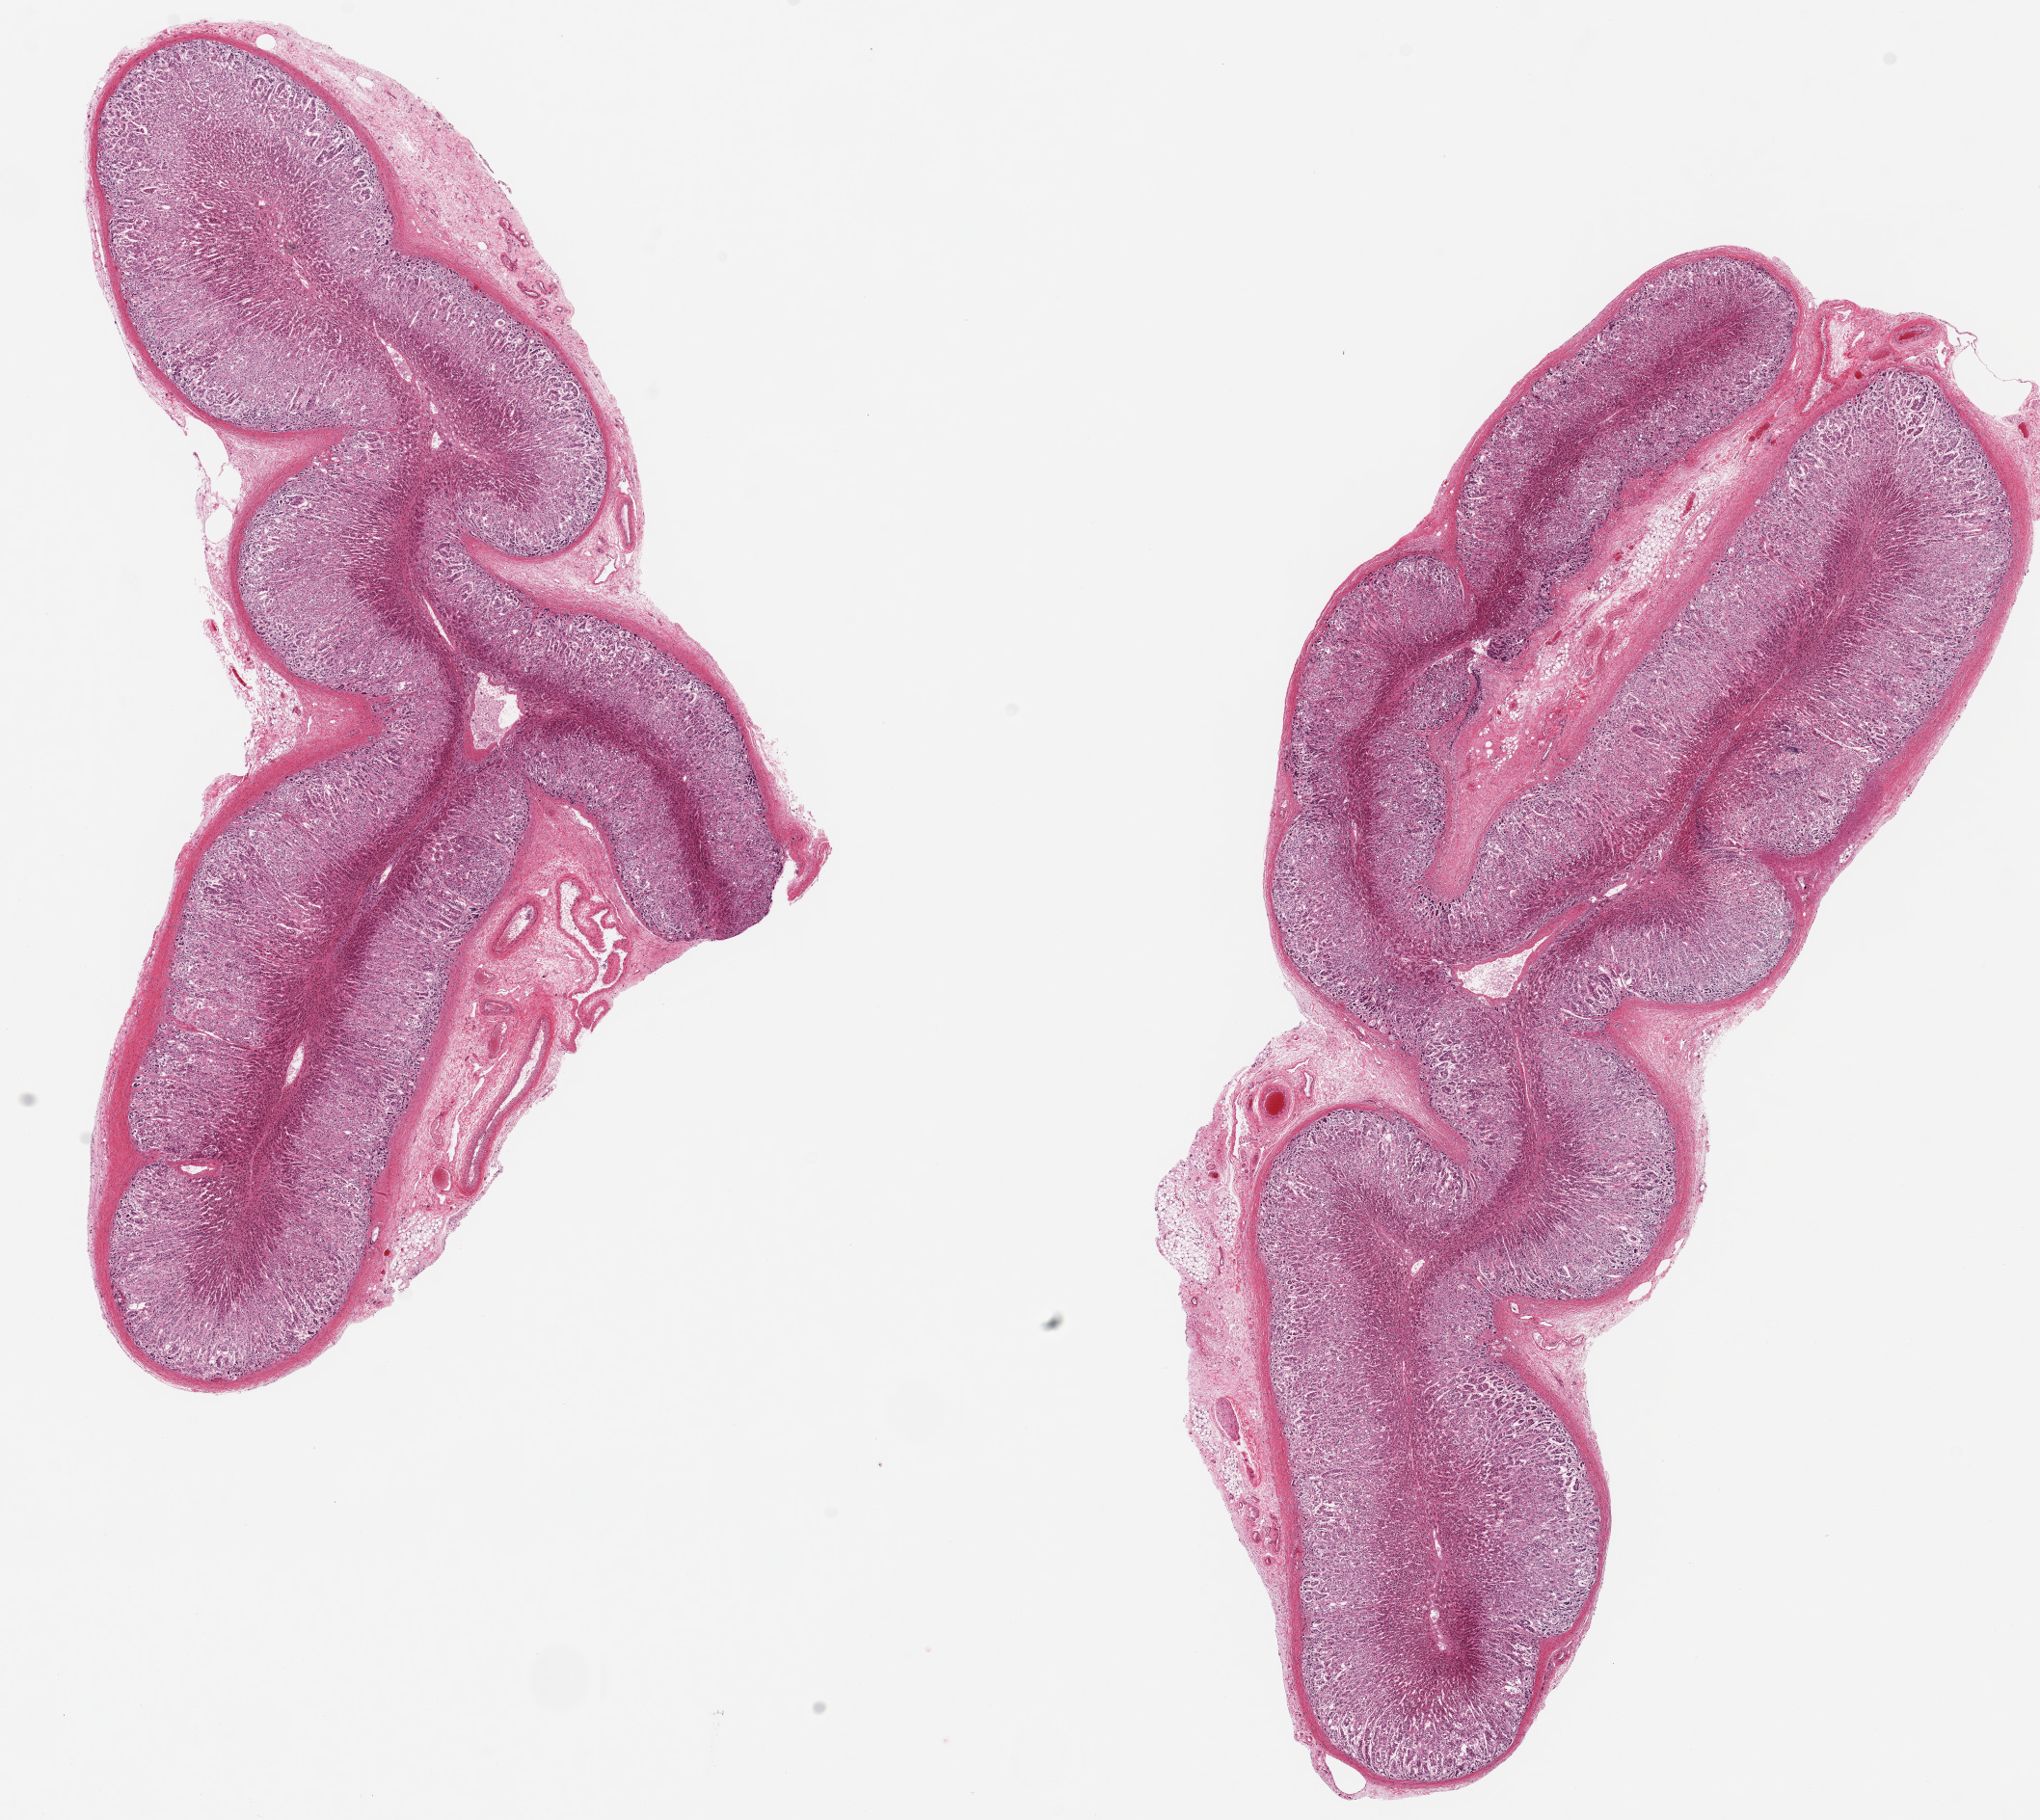
Digitized H&E-stained section, low-resolution overview of the scanned area, about 16.7 x 14.9 mm (from a 20x scan), PAXgene-fixed, paraffin-embedded tissue, sampled site (target tissue): adrenal gland, donor tissue sample.
Review note (as recorded): 2 pieces ~11x4mm. adherent fibroadipose/vascular tisssue delinieated, ~5% of both aliquots.